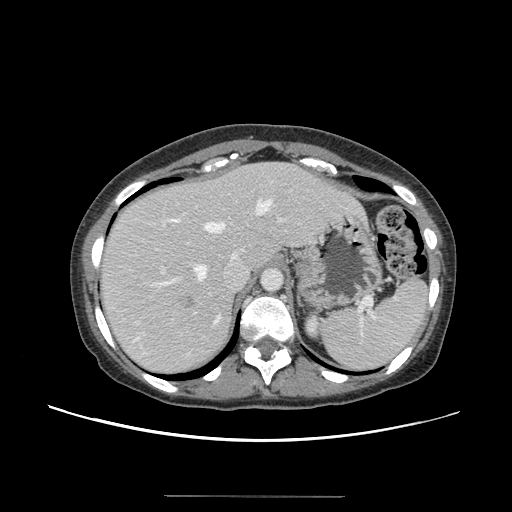
Contrast-enhanced abdominal CT, one axial slice; position 110 of 144 along the scan axis; 120 kVp; intravenous contrast given; soft-tissue window (W 400 / L 40 HU); 2.5 mm slice thickness; 512 × 512 image matrix, field of view 380 × 380 mm. Female patient, age 53 years. From the clinical record (not read from this slice): diagnosis: colorectal cancer liver metastases, imaged before liver resection.
Annotated regions visible in this slice (outlined manually by an expert reader):
- hepatic veins: bounding box (x1, y1, x2, y2) in pixels: (135, 201, 271, 340)
- liver: (101, 163, 363, 373)
- planned liver remnant (the part of the liver to remain after resection): (98, 163, 295, 301)
- portal vein (with intrahepatic branches): (161, 218, 285, 274)
- liver metastasis: (182, 296, 194, 308)